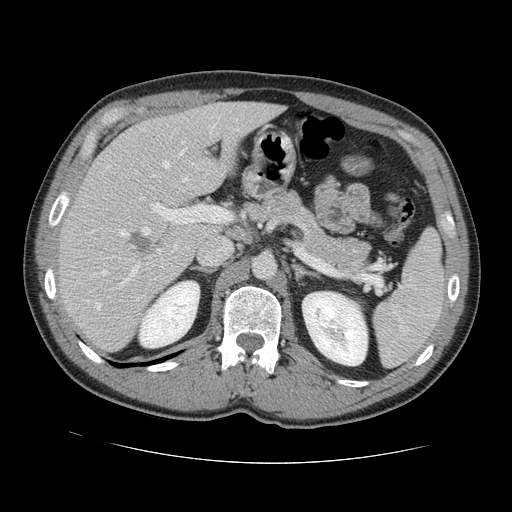
Contrast-enhanced abdominal CT, one axial slice; position 82 of 131 along the scan axis; intravenous contrast given; soft-tissue window (W 400 / L 40 HU); 2.5 mm slice thickness; 512 × 512 image matrix, field of view 380 × 380 mm. Male patient, age 40 years. From the clinical record (not read from this slice): diagnosis: colorectal cancer liver metastases, imaged before liver resection; multiple liver metastases: yes; largest metastasis: 2.9 cm; chemotherapy before resection: yes.
Annotated regions visible in this slice (expert manual segmentation):
- hepatic veins: bounding box (x1, y1, x2, y2) in pixels: (96, 147, 188, 309)
- liver: (61, 103, 280, 351)
- planned liver remnant (the part of the liver to remain after resection): (104, 102, 280, 199)
- portal vein (with intrahepatic branches): (112, 197, 232, 290)
- liver metastasis: (130, 232, 156, 257)